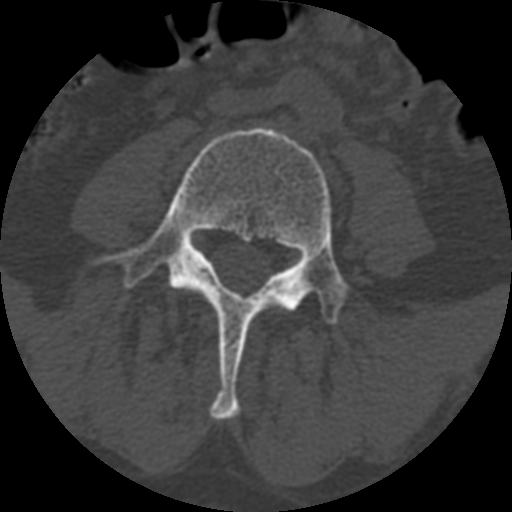
CT including the spine, one axial slice. Slice 282 of 399 in the series (ordered by position). 120 kVp. Bone window (W 1800 / L 400 HU). 512 × 512 image matrix, field of view 160 × 160 mm. Patient age 71 years. From the clinical record (not read from this slice): primary cancer: prostate.
Structures marked on this image (semi-automatic segmentation, software-assisted and operator-edited):
- L4 vertebra: bounding box <99,125,350,419> (left, top, right, bottom; pixels)